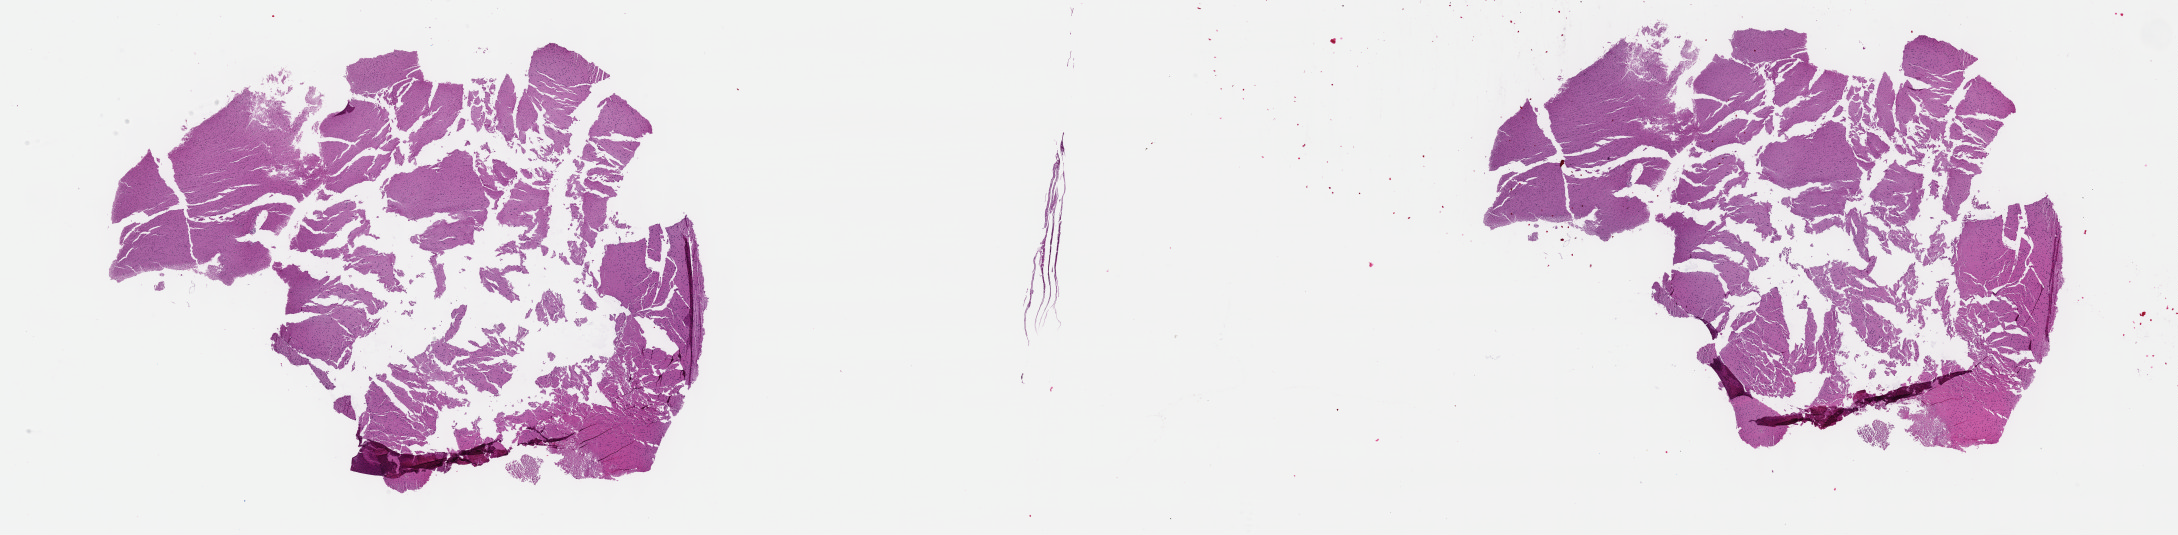
Whole-slide histology image, H&E-stained, low-resolution overview of the scanned area, about 35.2 x 8.7 mm, formalin-fixed paraffin-embedded (FFPE) diagnostic section, brain, primary tumour sample. Patient: female, age at initial diagnosis 74 years. Histologic grade: G2 (moderately differentiated).
Laterality: right. Diagnosis: Mixed glioma (cerebrum).